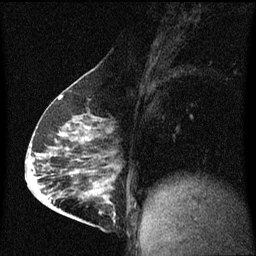
Breast MRI (dynamic contrast-enhanced), one sagittal slice; slice 30 of 60 in the series (ordered by position); dynamic contrast-enhanced series, image 2 of 3 at this slice position (ordered by acquisition); 1.5 T; TE 4.2 ms, TR 8 ms; 2 mm slice thickness; 256 × 256 image matrix. Female patient, age 63 years.
Annotated regions visible in this slice (semi-automatically segmented with operator editing):
- analysis volume of interest (the breast-tissue region the enhancement analysis was run in; not a lesion): box from (x=88, y=182) to (x=117, y=229) px
- tumour enhancement mask (voxels above the 70 % enhancement threshold inside the analysis volume of interest): (x=90, y=192)–(x=115, y=215)